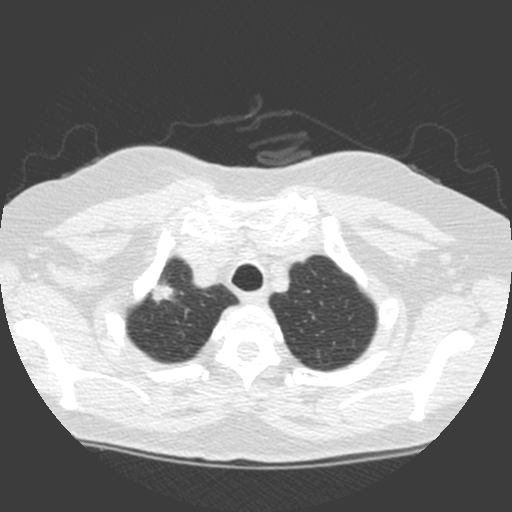
Axial slice from a low-dose chest CT screening exam, baseline annual screen, lung window (W 1500 / L -600 HU), standard (soft-tissue) reconstruction kernel (C), 512 × 512 image matrix. Female, age 63 years at enrolment. Current smoker at enrolment.
• Lesion marked by an expert reader, bounding box <139,273,182,309> (left, top, right, bottom; pixels).
• The exam's reader record, not a measurement of the box and not confirmed to be the same lesion: non-calcified nodule or mass ≥4 mm, right upper lobe, 11 × 11 mm, spiculated (stellate) margins, soft tissue attenuation.
• Official screen result: positive, change unspecified: nodule(s) >= 4 mm or enlarging nodule(s), mass(es), or other non-specific abnormalities suspicious for lung cancer.
• Later outcome: lung cancer diagnosed 6 days after this screen — adenocarcinoma, NOS, right upper lobe, poorly differentiated (G3), stage IA (AJCC 6th edition), 17 mm at pathology.